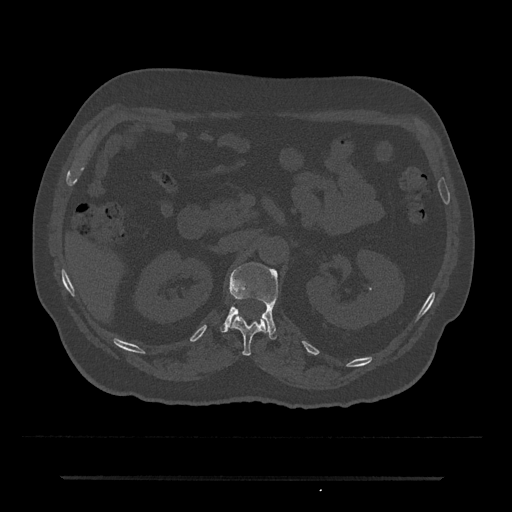
CT including the spine, one axial slice. Position 98 of 797 along the scan axis. Reconstruction kernel Br40s/3. 120 kVp. Bone window (W 1800 / L 400 HU). 0.5 mm slice thickness. 512 × 512 image matrix. Patient: male, 69 years. From the clinical record (not read from this slice): primary cancer: prostate.
Outlined on this slice (semi-automatic segmentation, software-assisted and operator-edited):
- L1 vertebra: box from (x=220, y=262) to (x=279, y=339) px
- T12 vertebra: (x=231, y=313)–(x=269, y=355)